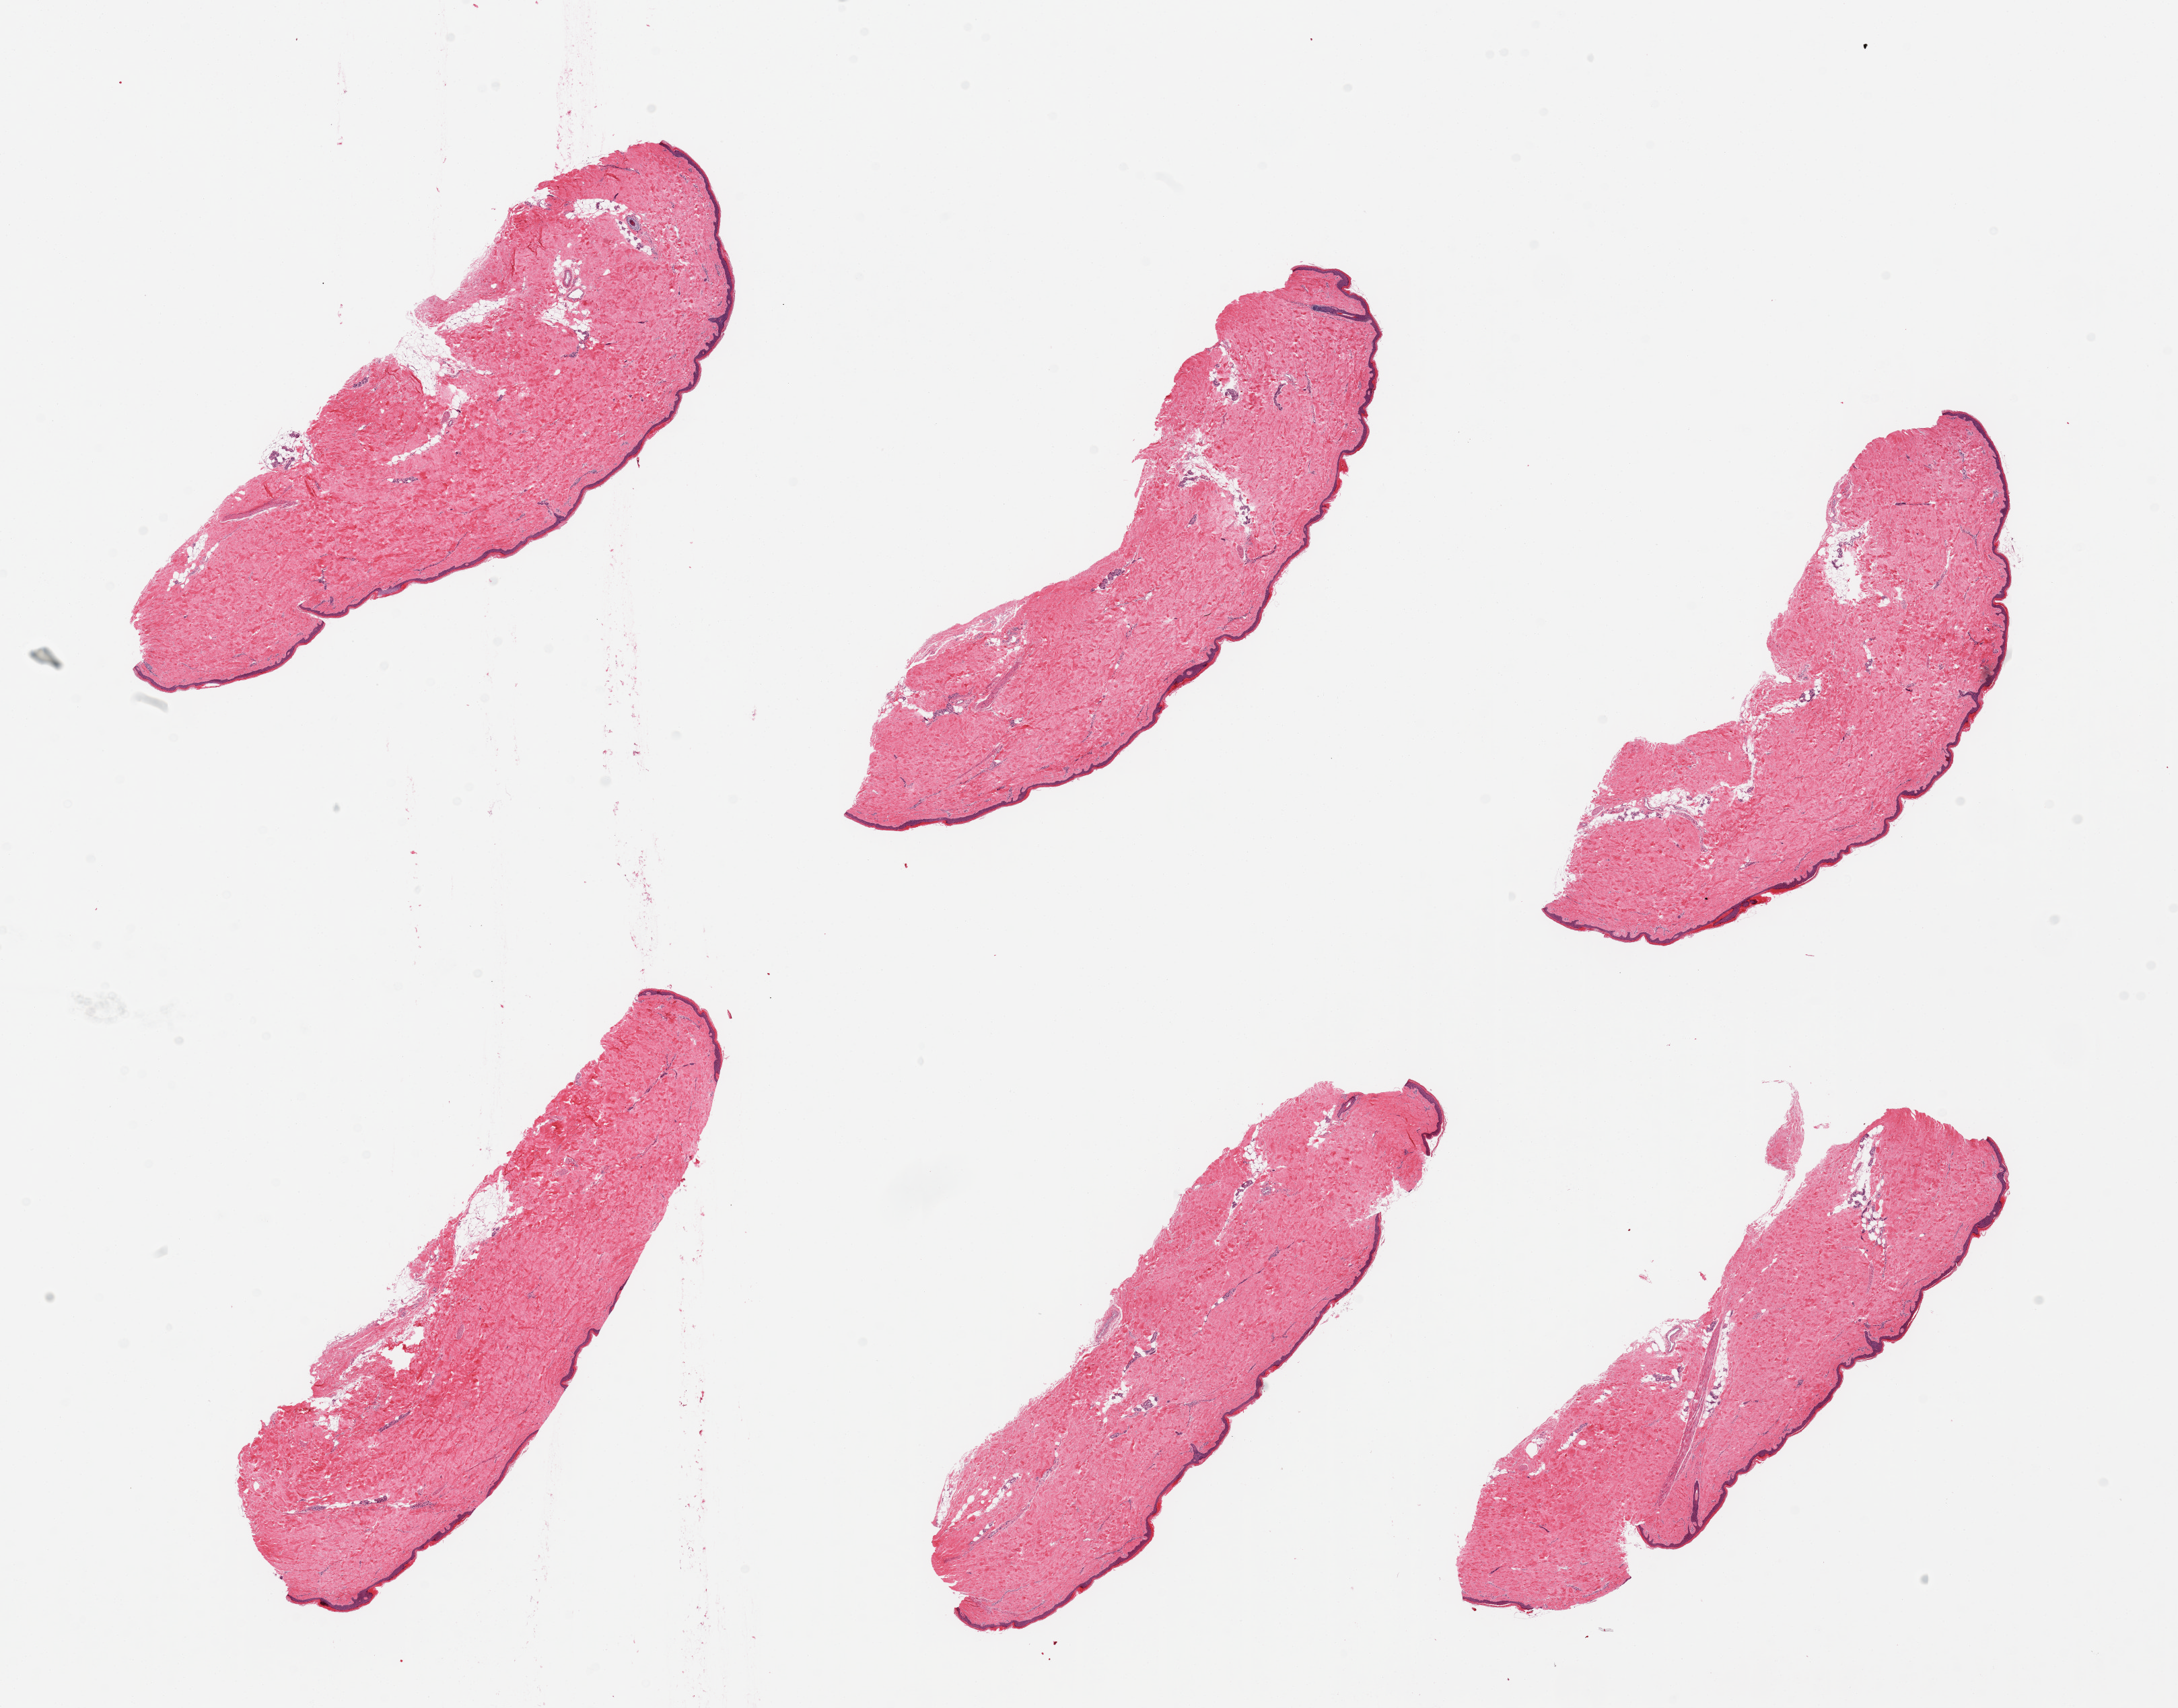
Haematoxylin and eosin whole-slide image — low-resolution overview of the scanned area, about 25.6 x 20.1 mm (slide scanned at 20x); PAXgene-fixed paraffin-embedded (PFPE) section; sampled site (target tissue): skin of lower leg; donor tissue sample. Female donor.
Reviewer comment on this tissue sample: 6 pieces, minimal dermal fat. Squamous epithelium is ~40 microns.